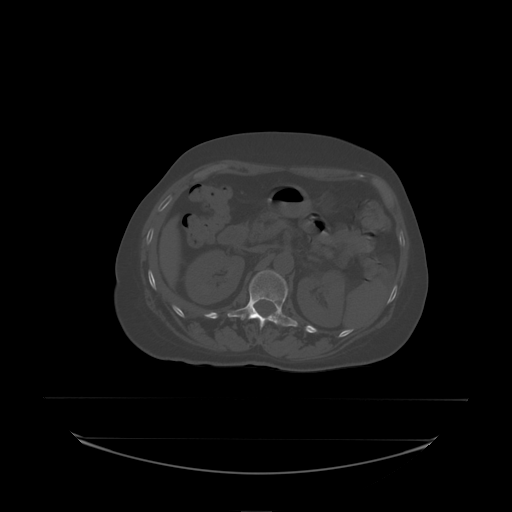
CT including the spine, one axial slice; slice 84 of 242 in the series (ordered by position); bone window (W 1800 / L 400 HU); 2.5 mm slice thickness; 512 × 512 image matrix, field of view 500 × 500 mm. Female patient, age 53 years. Case-level facts recorded for this patient, not image findings: primary cancer: lung; vertebrae with lytic lesions (as recorded): T7, L1.
Outlined on this slice (semi-automatic segmentation, software-assisted and operator-edited):
- L1 vertebra: bounding box [x1, y1, x2, y2] px = [228, 270, 298, 330]